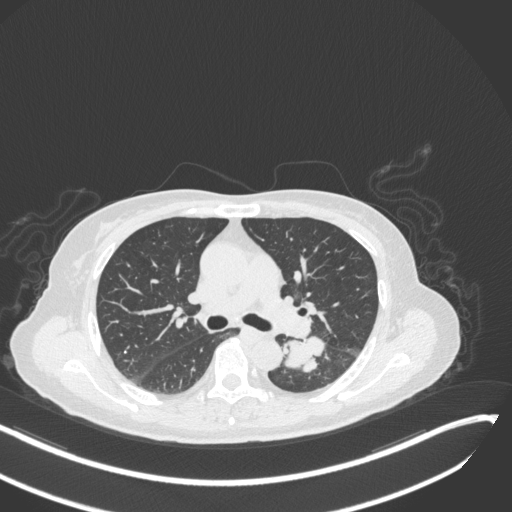
Chest CT, one axial slice; slice 173 of 342 in the series (ordered by position); reconstruction kernel B31f; lung window (W 1500 / L -600 HU); 512 × 512 image matrix, field of view 400 × 400 mm. Patient: female, 64 years. From the clinical record (not read from this slice): clinical TNM (as recorded): T3 N1 M1.
Annotated regions visible in this slice (bounding box drawn by a radiologist):
- lung tumour (recorded histology: small cell carcinoma): bounding box (x1, y1, x2, y2) in pixels: (276, 336, 330, 376)